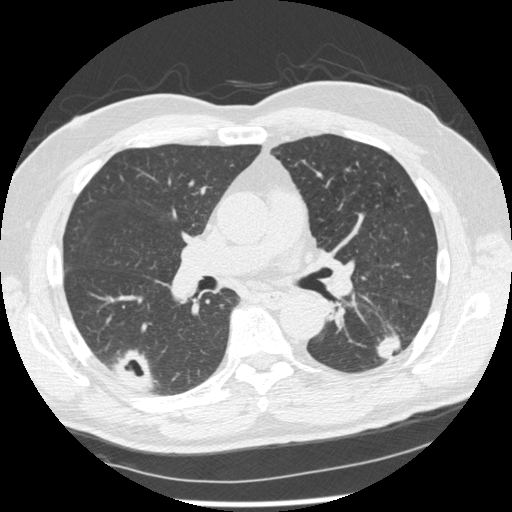
Chest CT (low-dose screening protocol), one axial image; second annual screen; lung window (W 1500 / L -600 HU); 1.25 mm slice thickness; standard (soft-tissue) reconstruction kernel (STANDARD); slice 112 of 227 in the series; 512 × 512 image matrix, field of view 360 × 360 mm. Male participant, aged 74 years at enrolment. Former smoker at enrolment.
Expert-annotated lung lesion, bounding box [x1, y1, x2, y2] px = [371, 316, 422, 369]. The screening reader recorded 7 non-calcified nodules or masses ≥4 mm on this exam (right upper lobe, right lower lobe, right upper lobe, right lower lobe, left lower lobe, left upper lobe, left upper lobe); which of them this box marks is not recorded.